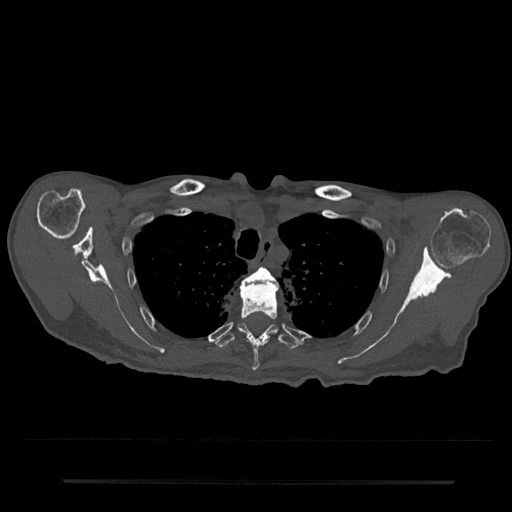
CT including the spine, one axial slice; position 609 of 797 along the scan axis; reconstruction kernel Br40s/3; 120 kVp; bone window (W 1800 / L 400 HU); 0.5 mm slice thickness; 512 × 512 image matrix, field of view 427 × 427 mm. Patient: male, 74 years. Case-level facts recorded for this patient, not image findings: primary cancer: prostate.
Structures marked on this image (semi-automatic segmentation, software-assisted and operator-edited):
- T3 vertebra: bounding box [x1, y1, x2, y2] px = [241, 267, 278, 289]
- T4 vertebra: [240, 282, 278, 371]
- T5 vertebra: [214, 323, 301, 350]